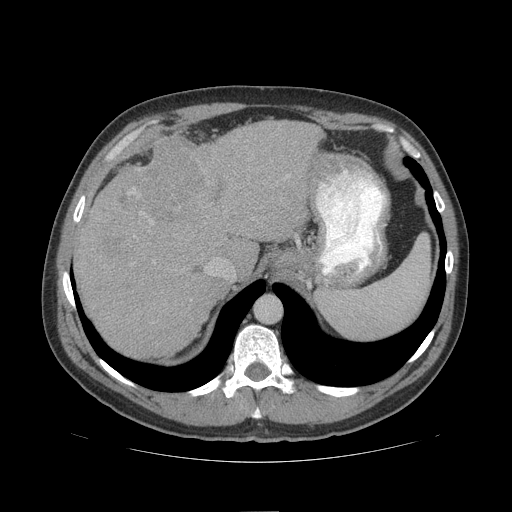
Contrast-enhanced abdominal CT (liver protocol), one axial slice; position 79 of 109 along the scan axis; reconstruction kernel STANDARD; 140 kVp; soft-tissue window (W 400 / L 40 HU); 512 × 512 image matrix, field of view 420 × 420 mm. From the clinical record (not read from this slice): diagnosis: hepatocellular carcinoma (patient treated with transarterial chemoembolisation; whether this scan precedes or follows treatment is not stated here); TNM stage (as recorded): Stage-IIIB; Child-Pugh class: A; tumour nodularity: multinodular.
Structures marked on this image (semi-automatically segmented with operator editing):
- abdominal aorta: bounding box <256,297,281,323> (left, top, right, bottom; pixels)
- liver parenchyma outside the tumour (the mass and vessels are separate outlines, so this box may not span the whole liver): <74,120,320,358>
- mass: <108,134,205,232>